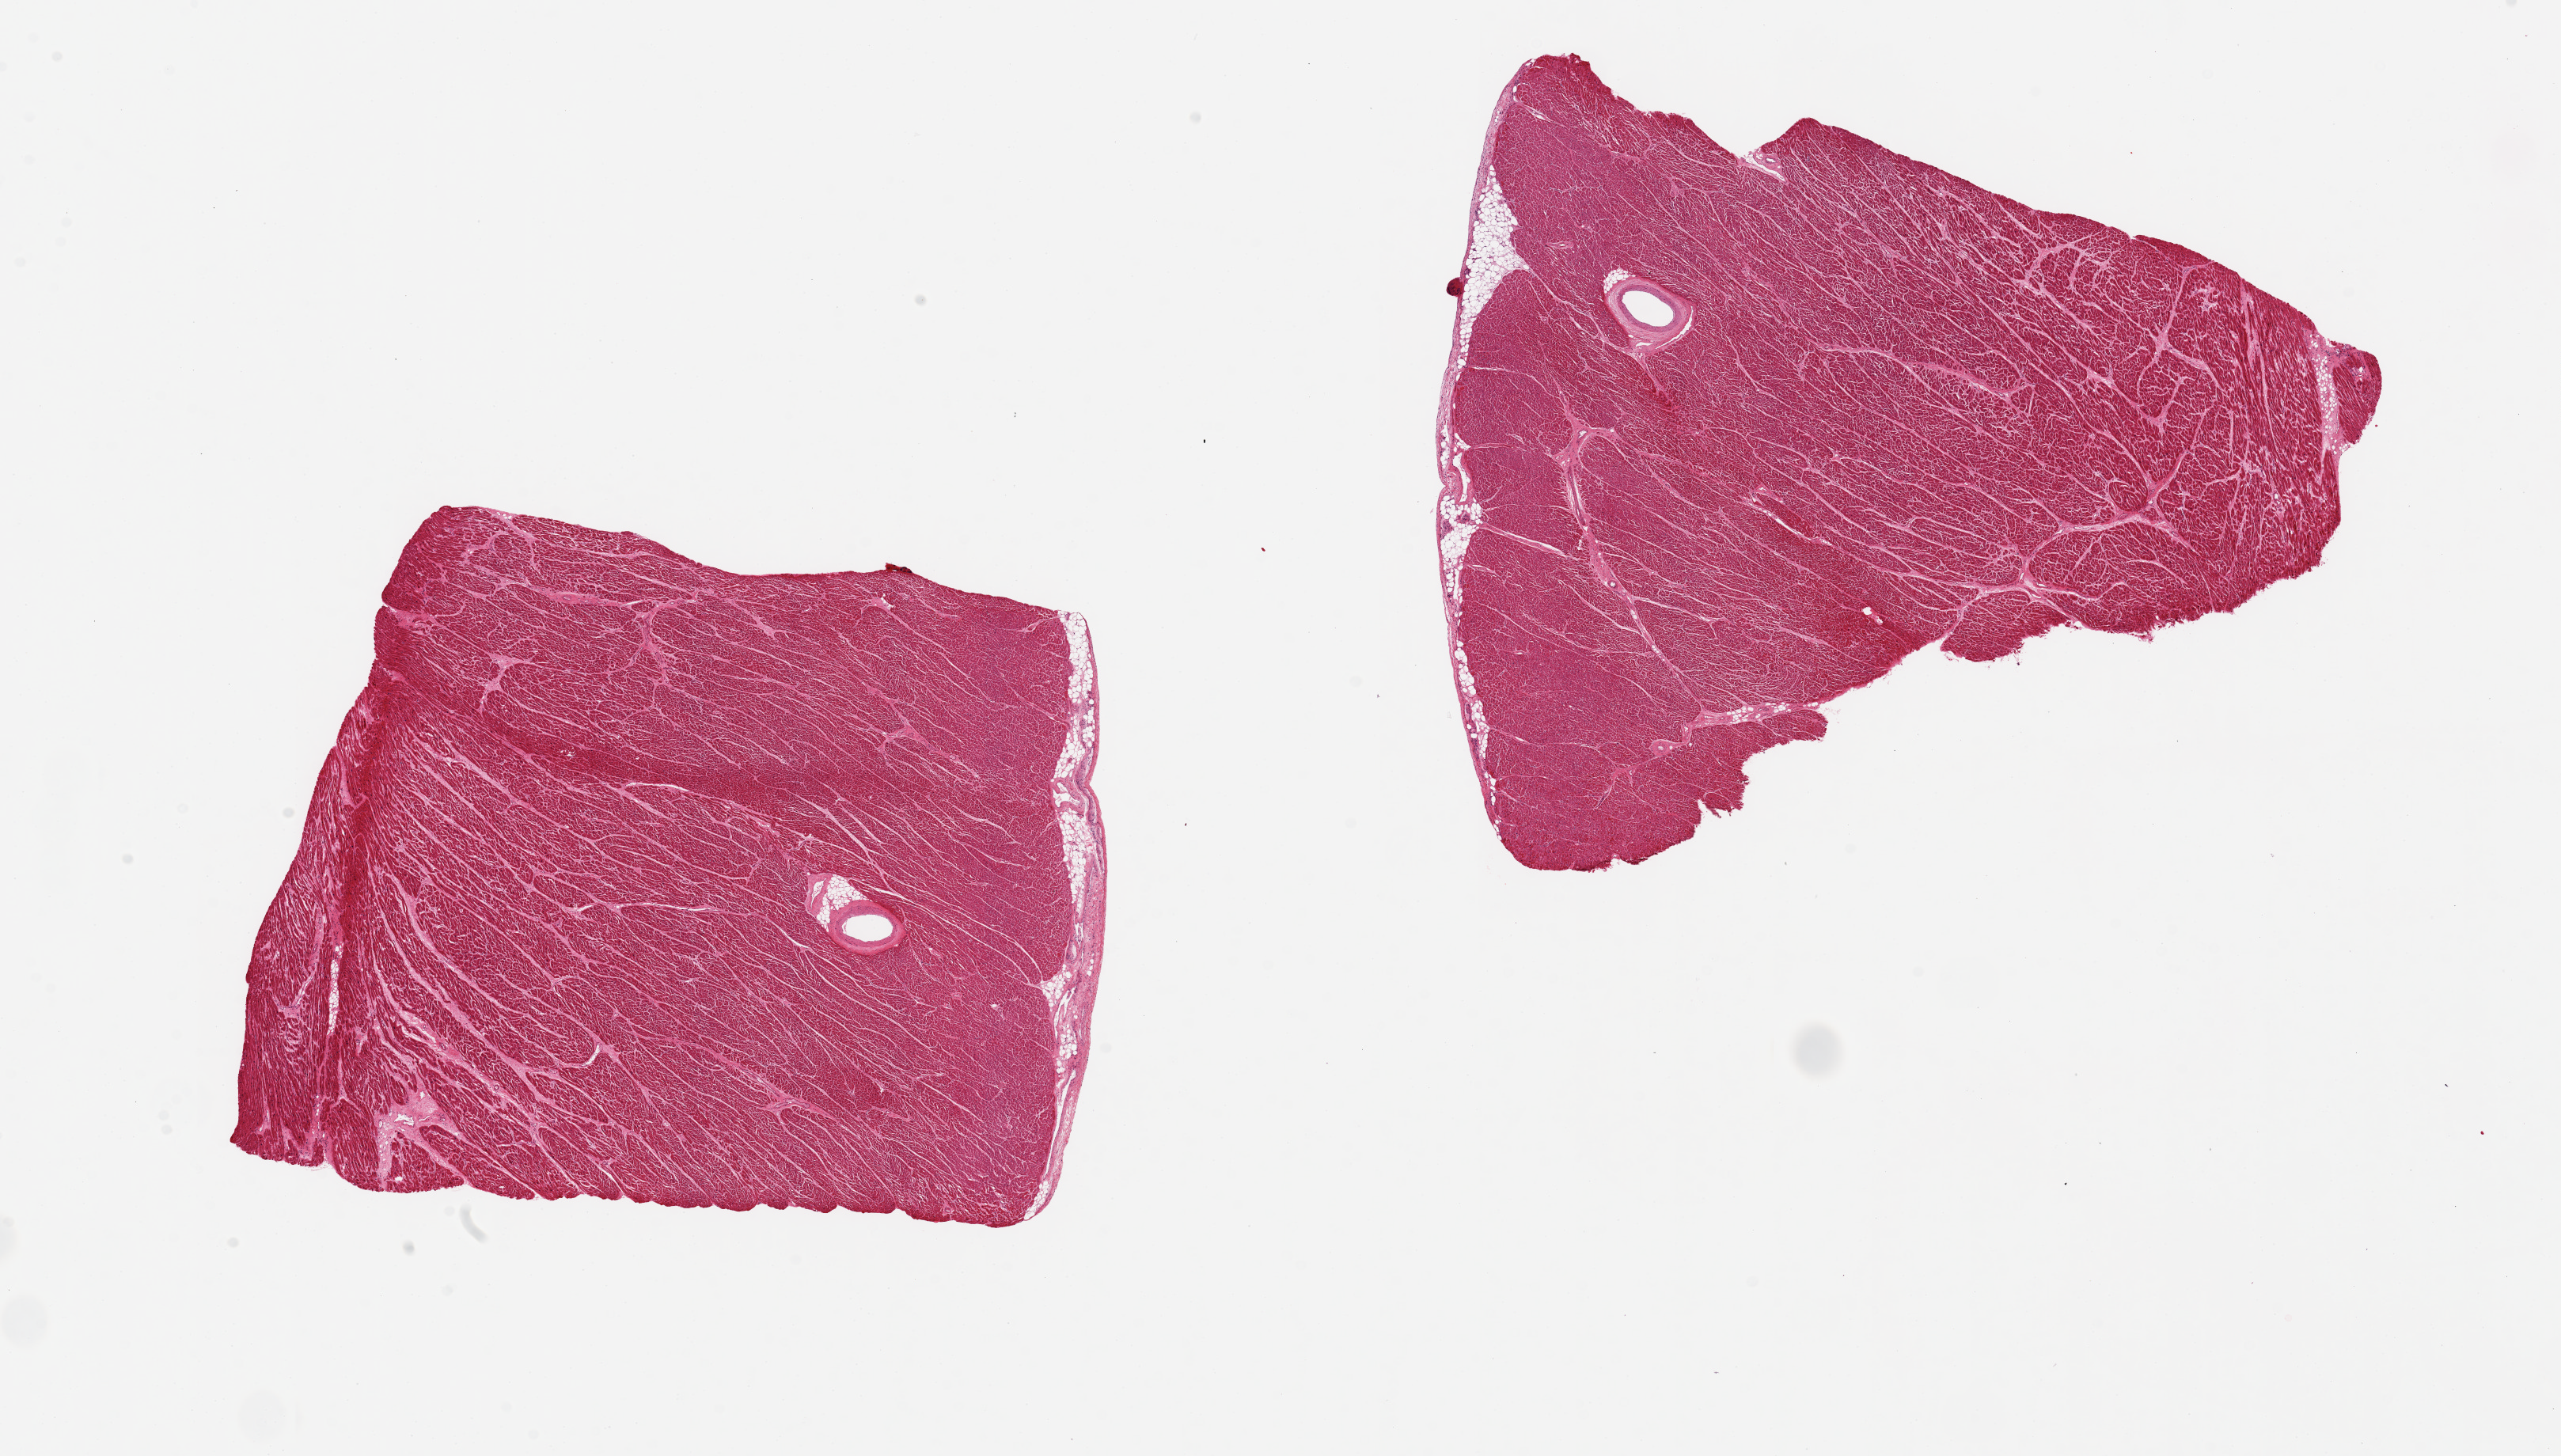
Whole-slide image, H&E stain — whole scanned area (about 25.6 x 14.6 mm, slide scanned at 20x) shown as a low-resolution overview. PAXgene-fixed, paraffin-embedded tissue. Section of heart (target tissue). Tissue donor sample. Donor: female.
Pathologist's review note for this sample: 2 pieces, 8x7 & 9.5x8mm; good specimen.